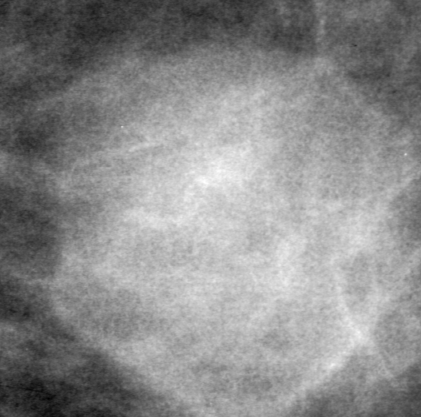
Region of interest cut from a scanned film mammogram (one marked finding); left breast; CC view; BI-RADS breast density category 2 (scale 1–4).
Marked abnormality: mass, shape lobulated, margins obscured; BI-RADS assessment category 4; subtlety rating 4 on a 1 (subtle) to 5 (obvious) scale; pathology result (as recorded, not read from the image): benign.